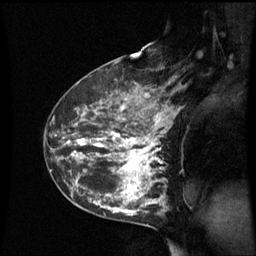
Breast MRI (dynamic contrast-enhanced), one sagittal slice; slice 36 of 60 in the series (ordered by position); dynamic contrast-enhanced series, image 2 of 3 at this slice position (ordered by acquisition); 1.5 T; TE 4.2 ms, TR 8.9 ms; 2.4 mm slice thickness; 256 × 256 image matrix, field of view 210 × 210 mm. Patient: female, 42 years. From the clinical record (not read from this slice): setting: breast cancer imaged before/during neoadjuvant chemotherapy; receptor status: HER2-positive.
Outlined on this slice (semi-automatically segmented with operator editing):
- analysis volume of interest (the breast-tissue region the enhancement analysis was run in; not a lesion): bounding box (x1, y1, x2, y2) in pixels: (62, 93, 171, 210)
- tumour enhancement mask (voxels above the 70 % enhancement threshold inside the analysis volume of interest): (68, 95, 167, 210)